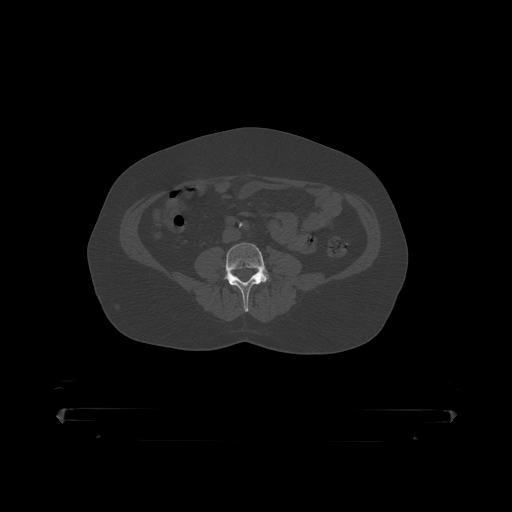
CT including the spine, one axial slice; slice 63 of 390 in the series (ordered by position); reconstruction kernel STANDARD; 120 kVp; bone window (W 1800 / L 400 HU); 1.25 mm slice thickness; 512 × 512 image matrix, field of view 650 × 650 mm. Patient: male, 60 years. Case-level facts recorded for this patient, not image findings: primary cancer: prostate.
Structures marked on this image (semi-automatically segmented with operator editing):
- L4 vertebra: bounding box <221,243,273,312> (left, top, right, bottom; pixels)